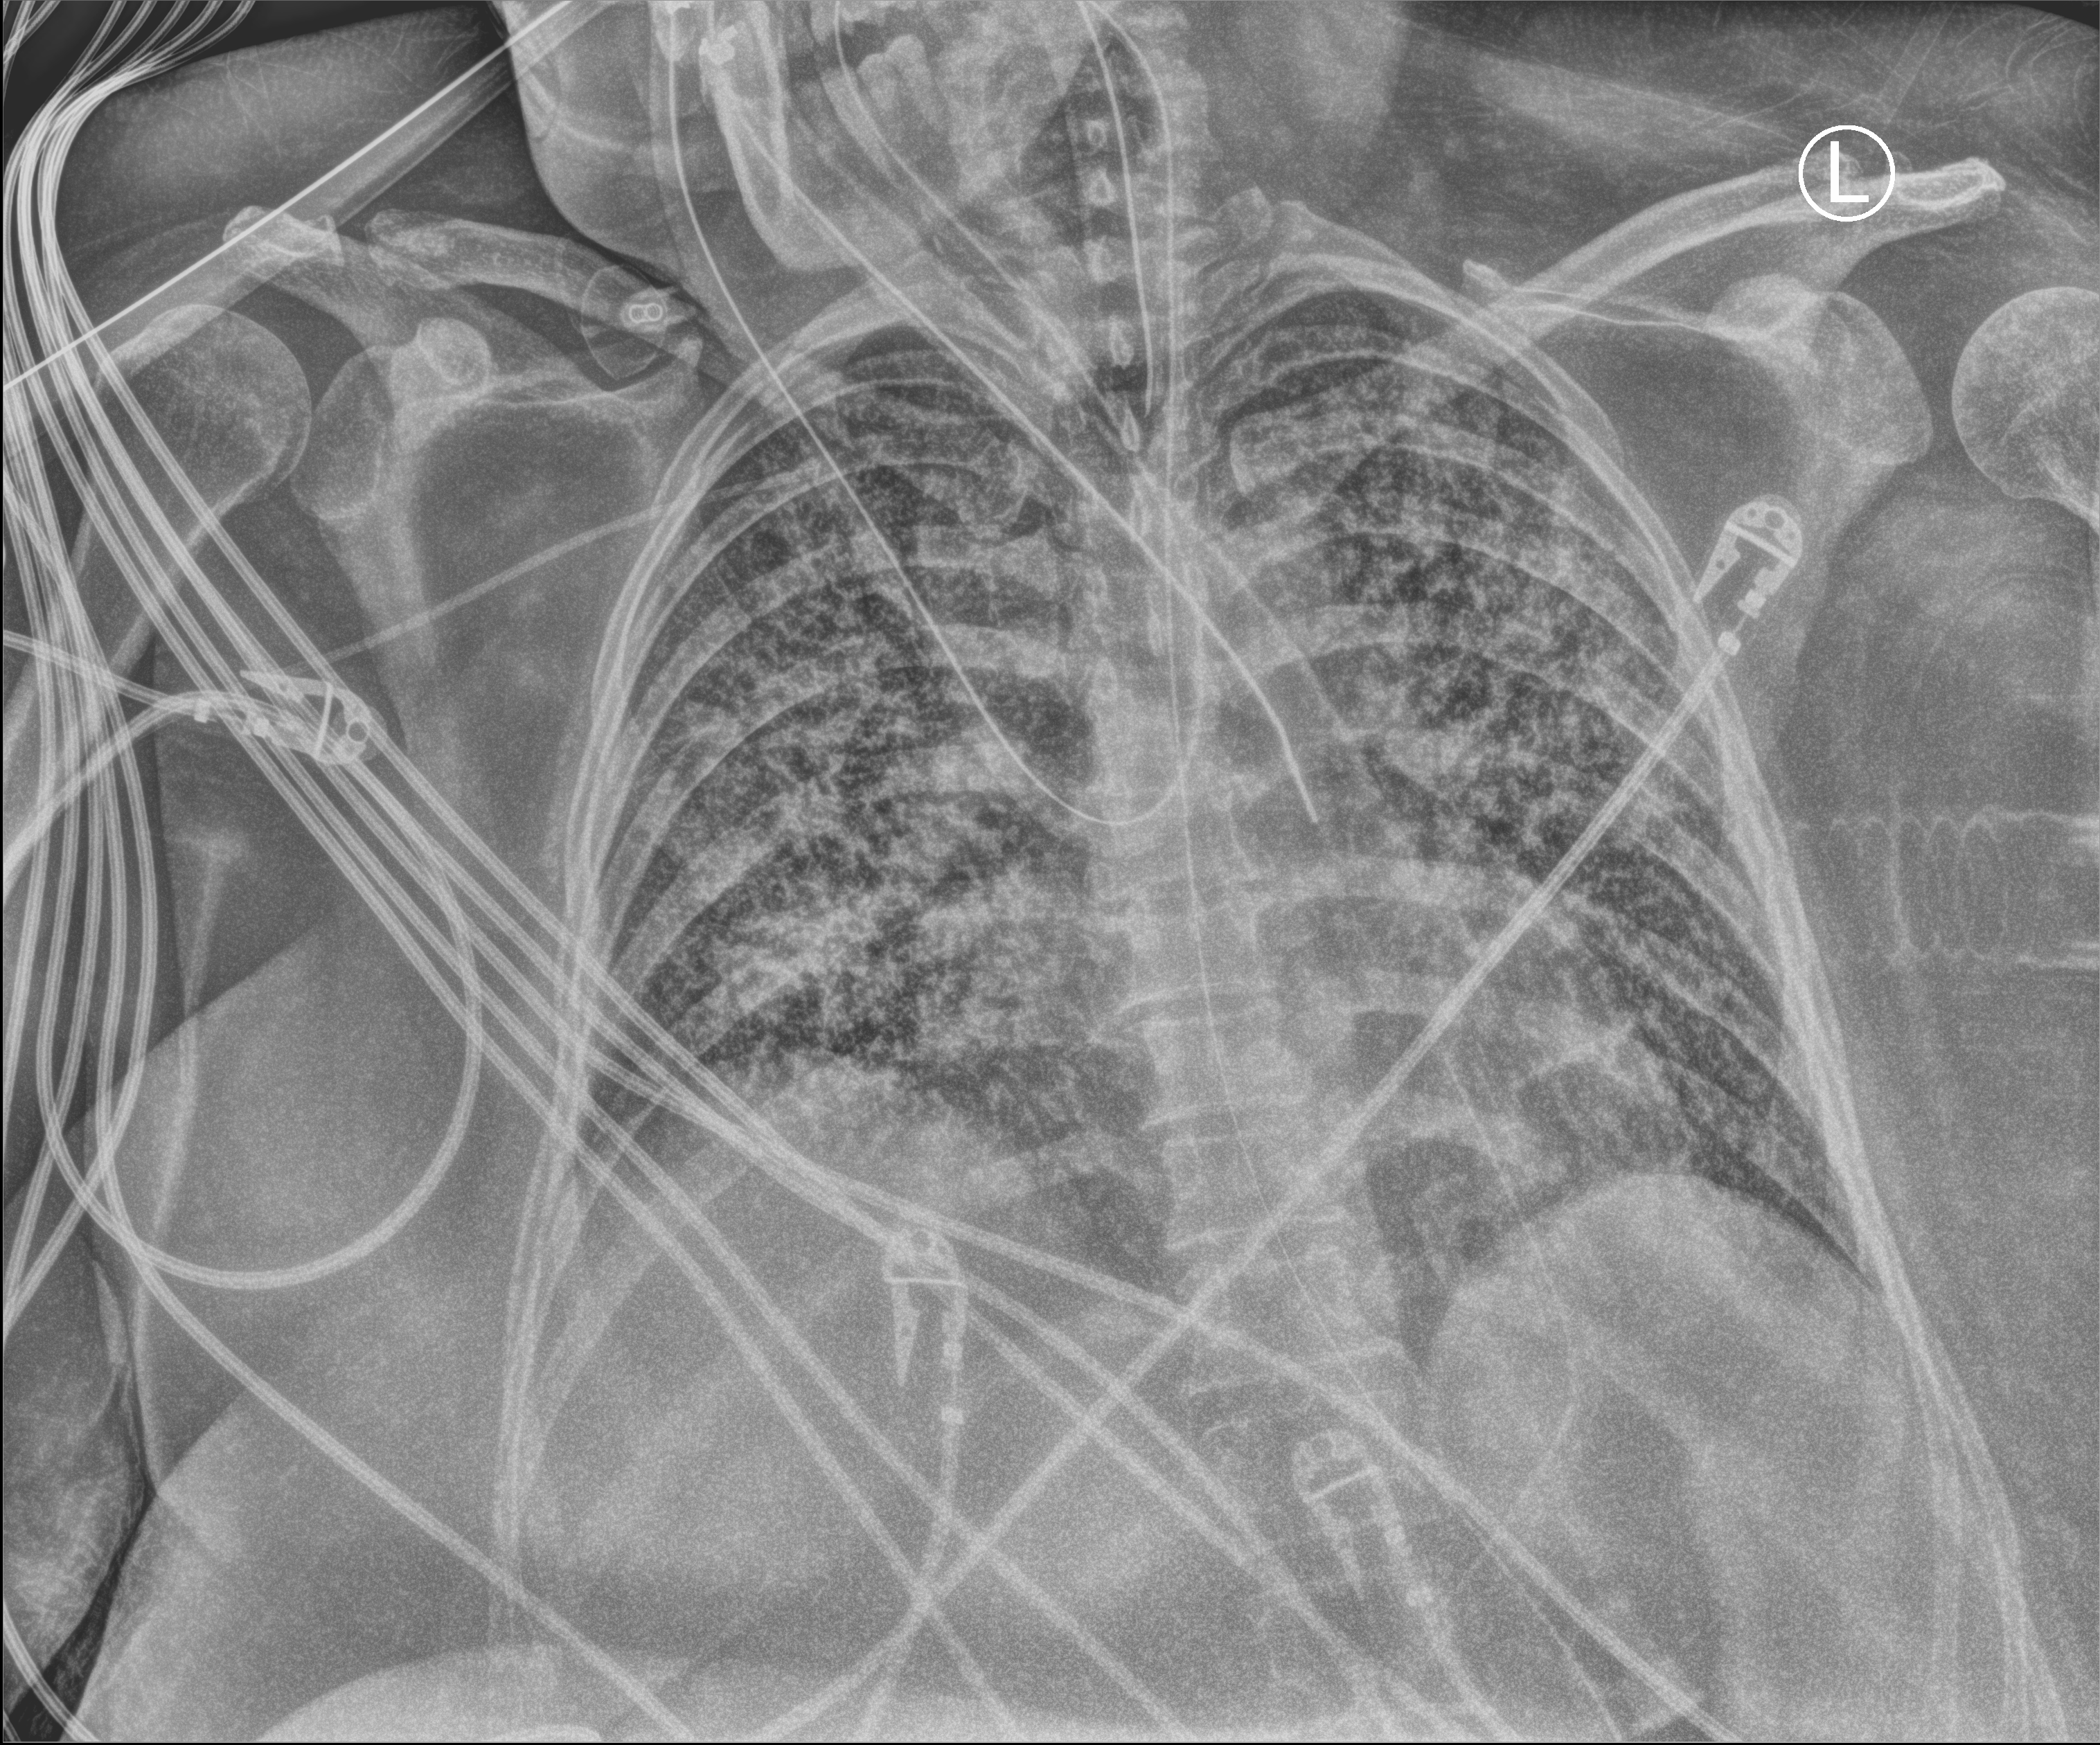
Bedside chest radiograph (computed radiography), anteroposterior (AP) projection. Female patient hospitalised with COVID-19, age 18–59 years.
Hospital-stay facts (about this admission, not read from this image; timing relative to this image not recorded): mechanically ventilated during this hospital stay: yes; admitted to intensive care during this hospital stay: yes.